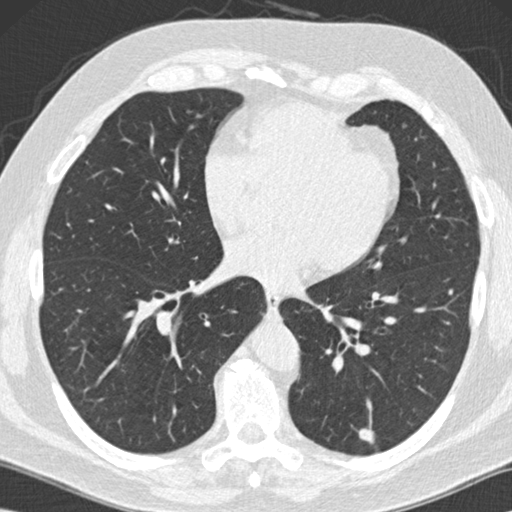
Low-dose screening chest CT, one axial slice. Position 59 of 152 along the scan axis. Lung window (W 1500 / L -600 HU). 512 × 512 image matrix, field of view 350 × 350 mm.
Outlined on this slice (manually delineated by an expert):
- lesion 1 (tumor, lower lobe of left lung): bounding box [x1, y1, x2, y2] px = [359, 426, 374, 444]